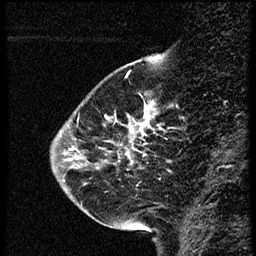
Breast MRI (dynamic contrast-enhanced), one sagittal slice. Slice 13 of 56 in the series (ordered by position). Dynamic contrast-enhanced study with each time point stored as its own series, time point 2 of 4 at this slice position (early post-contrast, ordered by acquisition time). 1.5 T. TE 4.2 ms, TR 18.9 ms. 256 × 256 image matrix, field of view 200 × 200 mm. Female patient. Case-level facts recorded for this patient, not image findings: setting: breast cancer imaged before/during neoadjuvant chemotherapy; receptor status: HER2-positive.
Outlined on this slice (semi-automatic segmentation, software-assisted and operator-edited):
- analysis volume of interest (the breast-tissue region the enhancement analysis was run in; not a lesion): bounding box (x1, y1, x2, y2) in pixels: (63, 80, 169, 215)
- tumour enhancement mask (voxels above the 100 % enhancement threshold inside the analysis volume of interest): (128, 106, 148, 157)